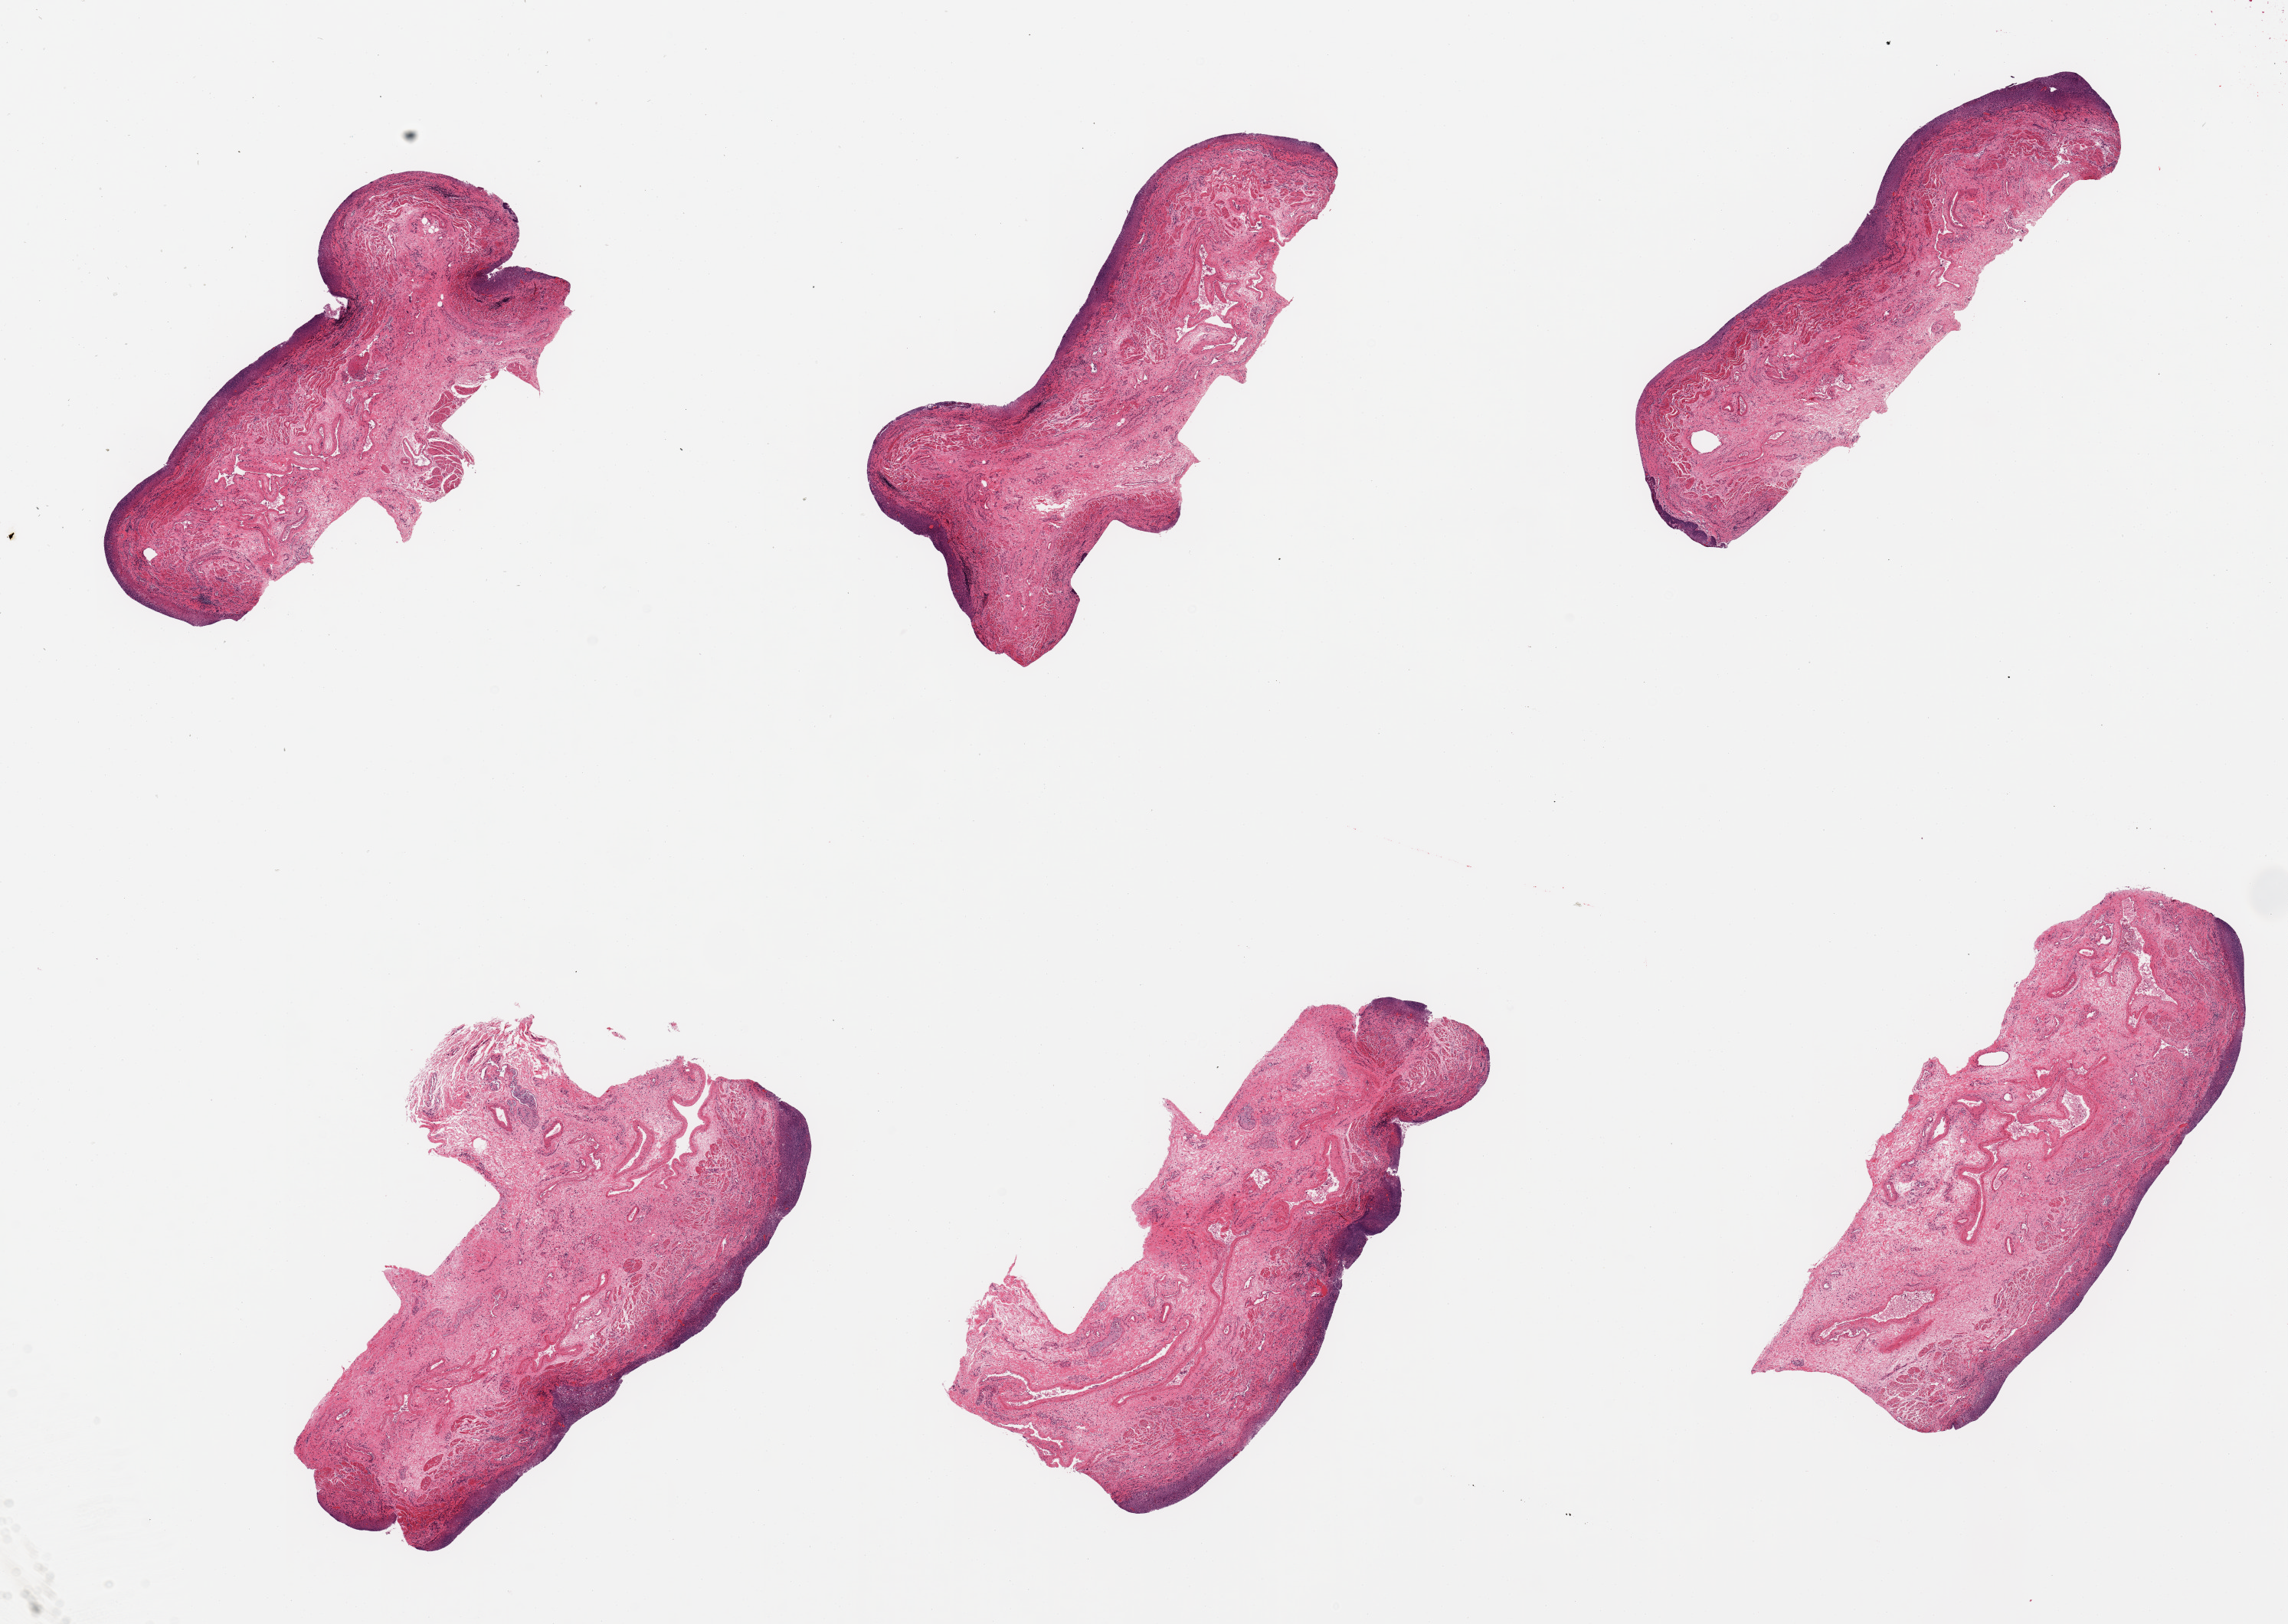
Hematoxylin and eosin (H&E) whole-slide image, brightfield — whole scanned area (about 23.6 x 16.8 mm, acquisition: 20x scan) shown as a low-resolution overview, PAXgene-fixed, paraffin-embedded tissue, sampled site (target tissue): esophageal mucous membrane, tissue donor sample. Male donor.
Pathologist's review note for this sample: 6 pieces; epithelium severely autolyzed; muscularis mucosae too dispersed for adequate sampling.